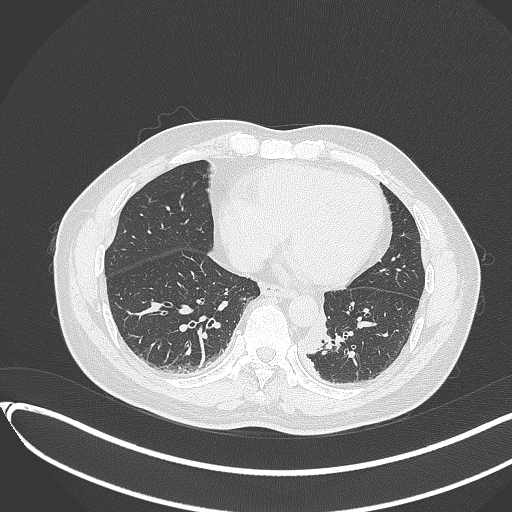
Chest CT, one axial slice. Position 108 of 417 along the scan axis. Reconstruction kernel B70f. Lung window (W 1500 / L -600 HU). 1 mm slice thickness. 512 × 512 image matrix, field of view 400 × 400 mm. Male patient, age 54 years. Case-level facts recorded for this patient, not image findings: clinical TNM (as recorded): T3 N0 M0.
Structures marked on this image (rectangle marked by the reading radiologist):
- lung tumour (recorded histology: squamous cell carcinoma): box from (x=298, y=309) to (x=331, y=357) px